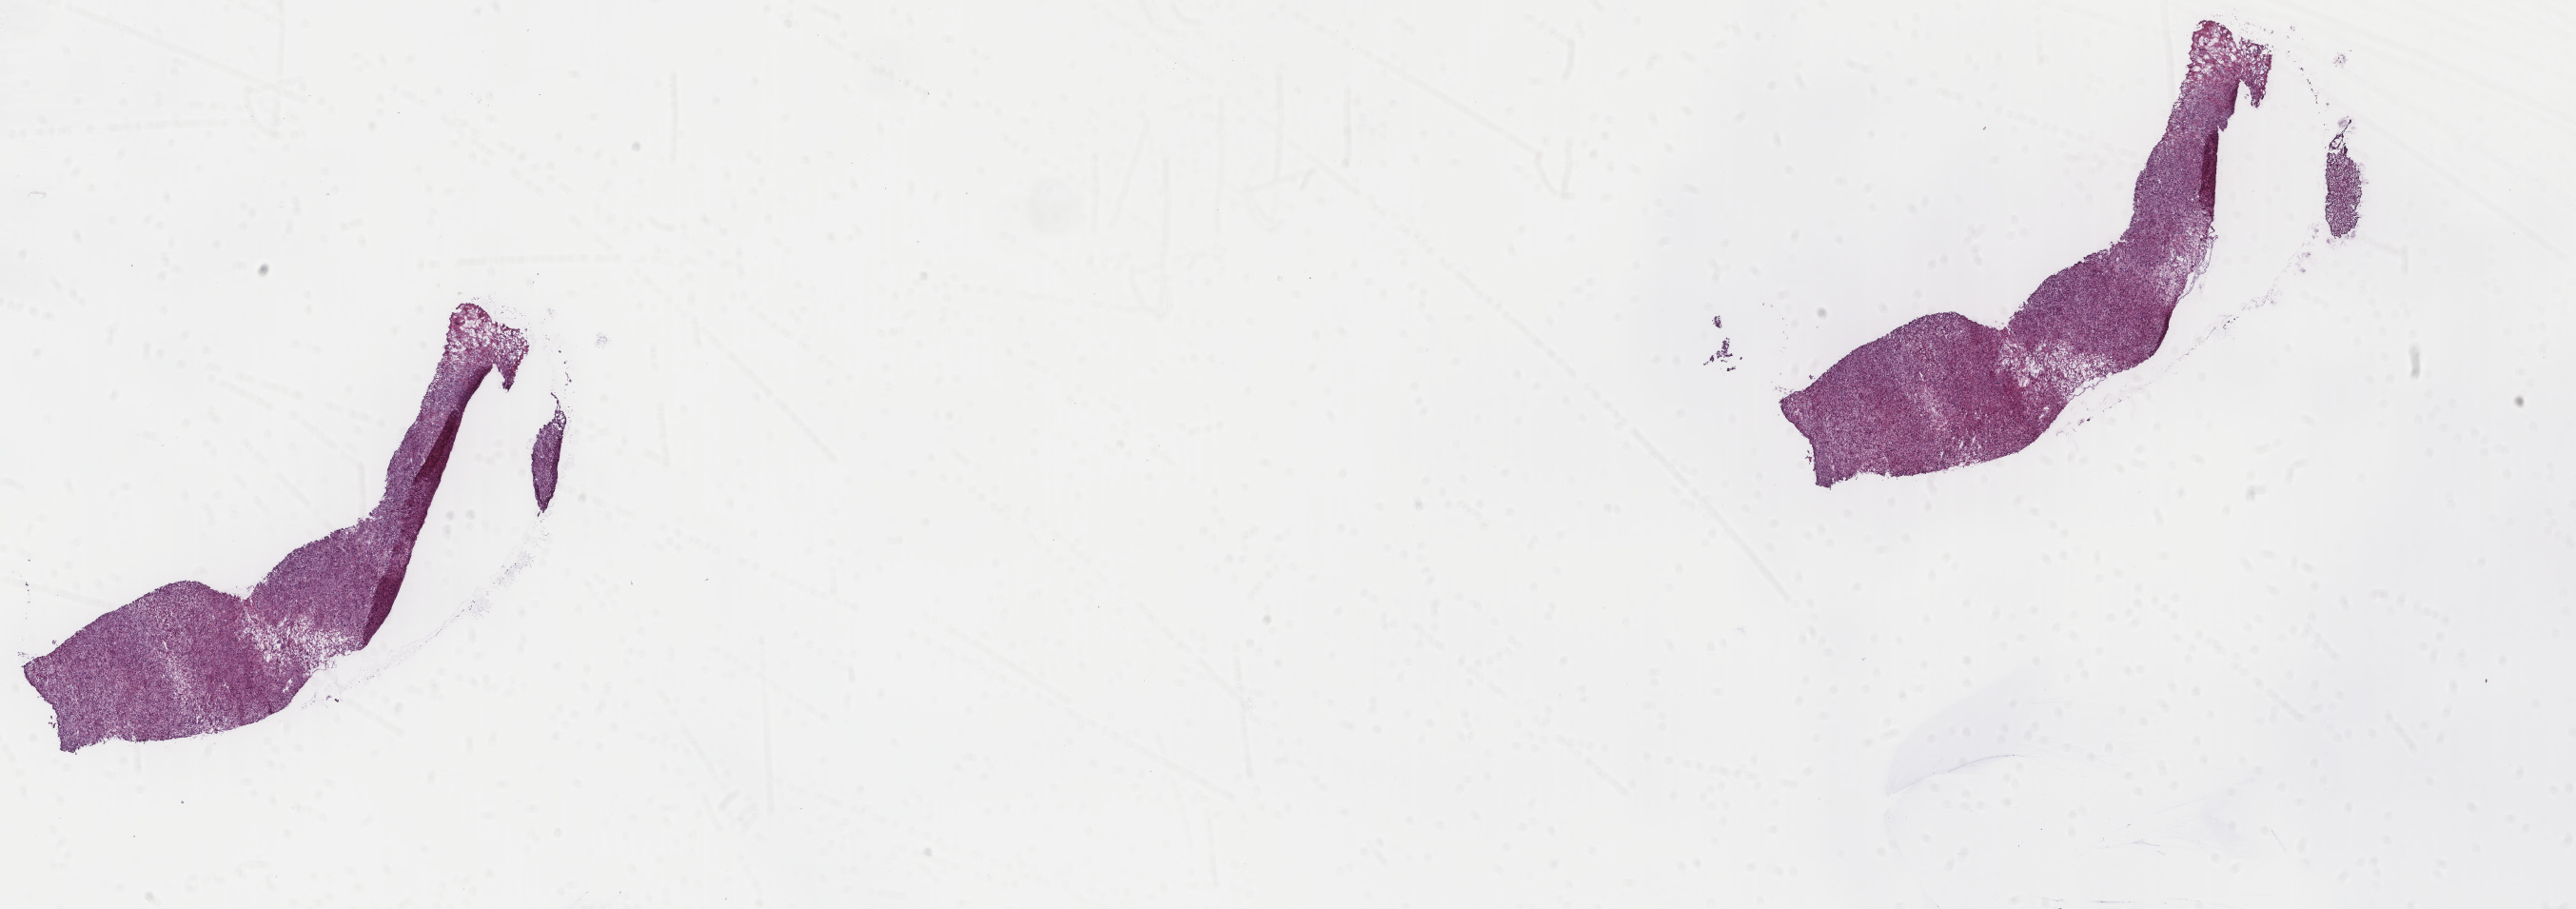
Hematoxylin and eosin (H&E) stained whole-slide image — shown as a low-resolution overview of the whole scanned area (about 21.5 x 7.6 mm, acquisition: 40x scan); frozen section; sample: primary tumour, retroperitoneum and peritoneum. Female, age 67 years at initial diagnosis. Slide review estimates, as recorded: tumour cells 85%, tumour nuclei 100%, normal cells 0%, stromal cells 15%, necrosis 0%. Inflammatory infiltration, as recorded: lymphocyte infiltration 0%, monocyte infiltration 0%, neutrophil infiltration 0%.
- pathologic diagnosis: Leiomyosarcoma, NOS (retroperitoneum)